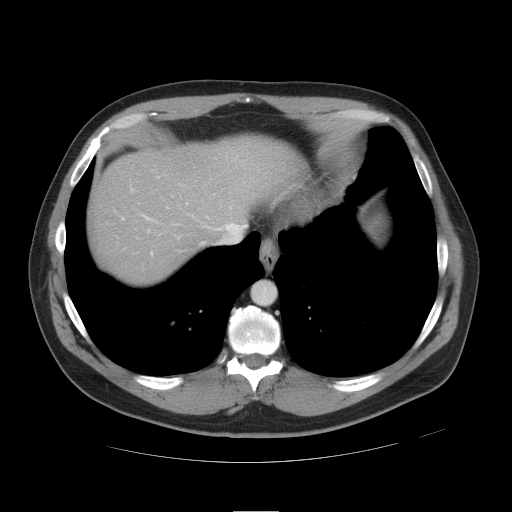
Contrast-enhanced abdominal CT, one axial slice. Position 41 of 49 along the scan axis. Reconstruction kernel STANDARD. Intravenous contrast given. Soft-tissue window (W 400 / L 40 HU). 5 mm slice thickness. 512 × 512 image matrix, field of view 425 × 425 mm. Male patient, age 52 years. Case-level facts recorded for this patient, not image findings: diagnosis: colorectal cancer liver metastases, imaged before liver resection; multiple liver metastases: yes; largest metastasis: 5.1 cm.
Structures marked on this image (outlined manually by an expert reader):
- hepatic veins: bounding box (x1, y1, x2, y2) in pixels: (146, 206, 246, 234)
- liver: (93, 142, 294, 282)
- planned liver remnant (the part of the liver to remain after resection): (142, 141, 295, 229)
- portal vein (with intrahepatic branches): (122, 187, 152, 255)